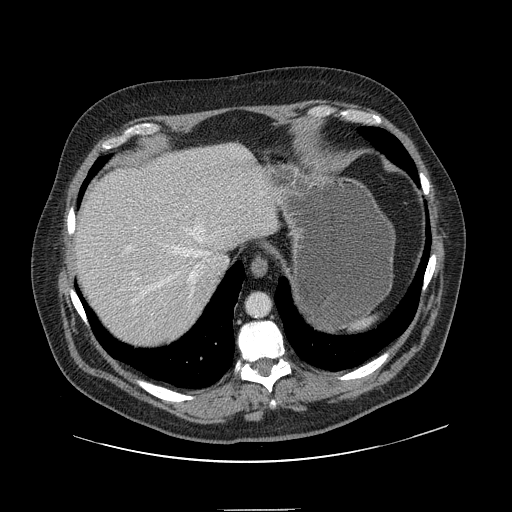
Contrast-enhanced abdominal CT, one axial slice. Slice 122 of 154 in the series (ordered by position). 120 kVp. Intravenous contrast given. Soft-tissue window (W 400 / L 40 HU). 2.5 mm slice thickness. 512 × 512 image matrix. Male patient, age 61 years. From the clinical record (not read from this slice): diagnosis: colorectal cancer liver metastases, imaged before liver resection; multiple liver metastases: yes; largest metastasis: 2.6 cm; disease in both lobes: yes.
Annotated regions visible in this slice (manually delineated by an expert):
- hepatic veins: box from (x=119, y=214) to (x=209, y=303) px
- liver: (x=75, y=145)–(x=277, y=350)
- planned liver remnant (the part of the liver to remain after resection): (x=75, y=145)–(x=276, y=347)
- portal vein (with intrahepatic branches): (x=132, y=227)–(x=137, y=281)